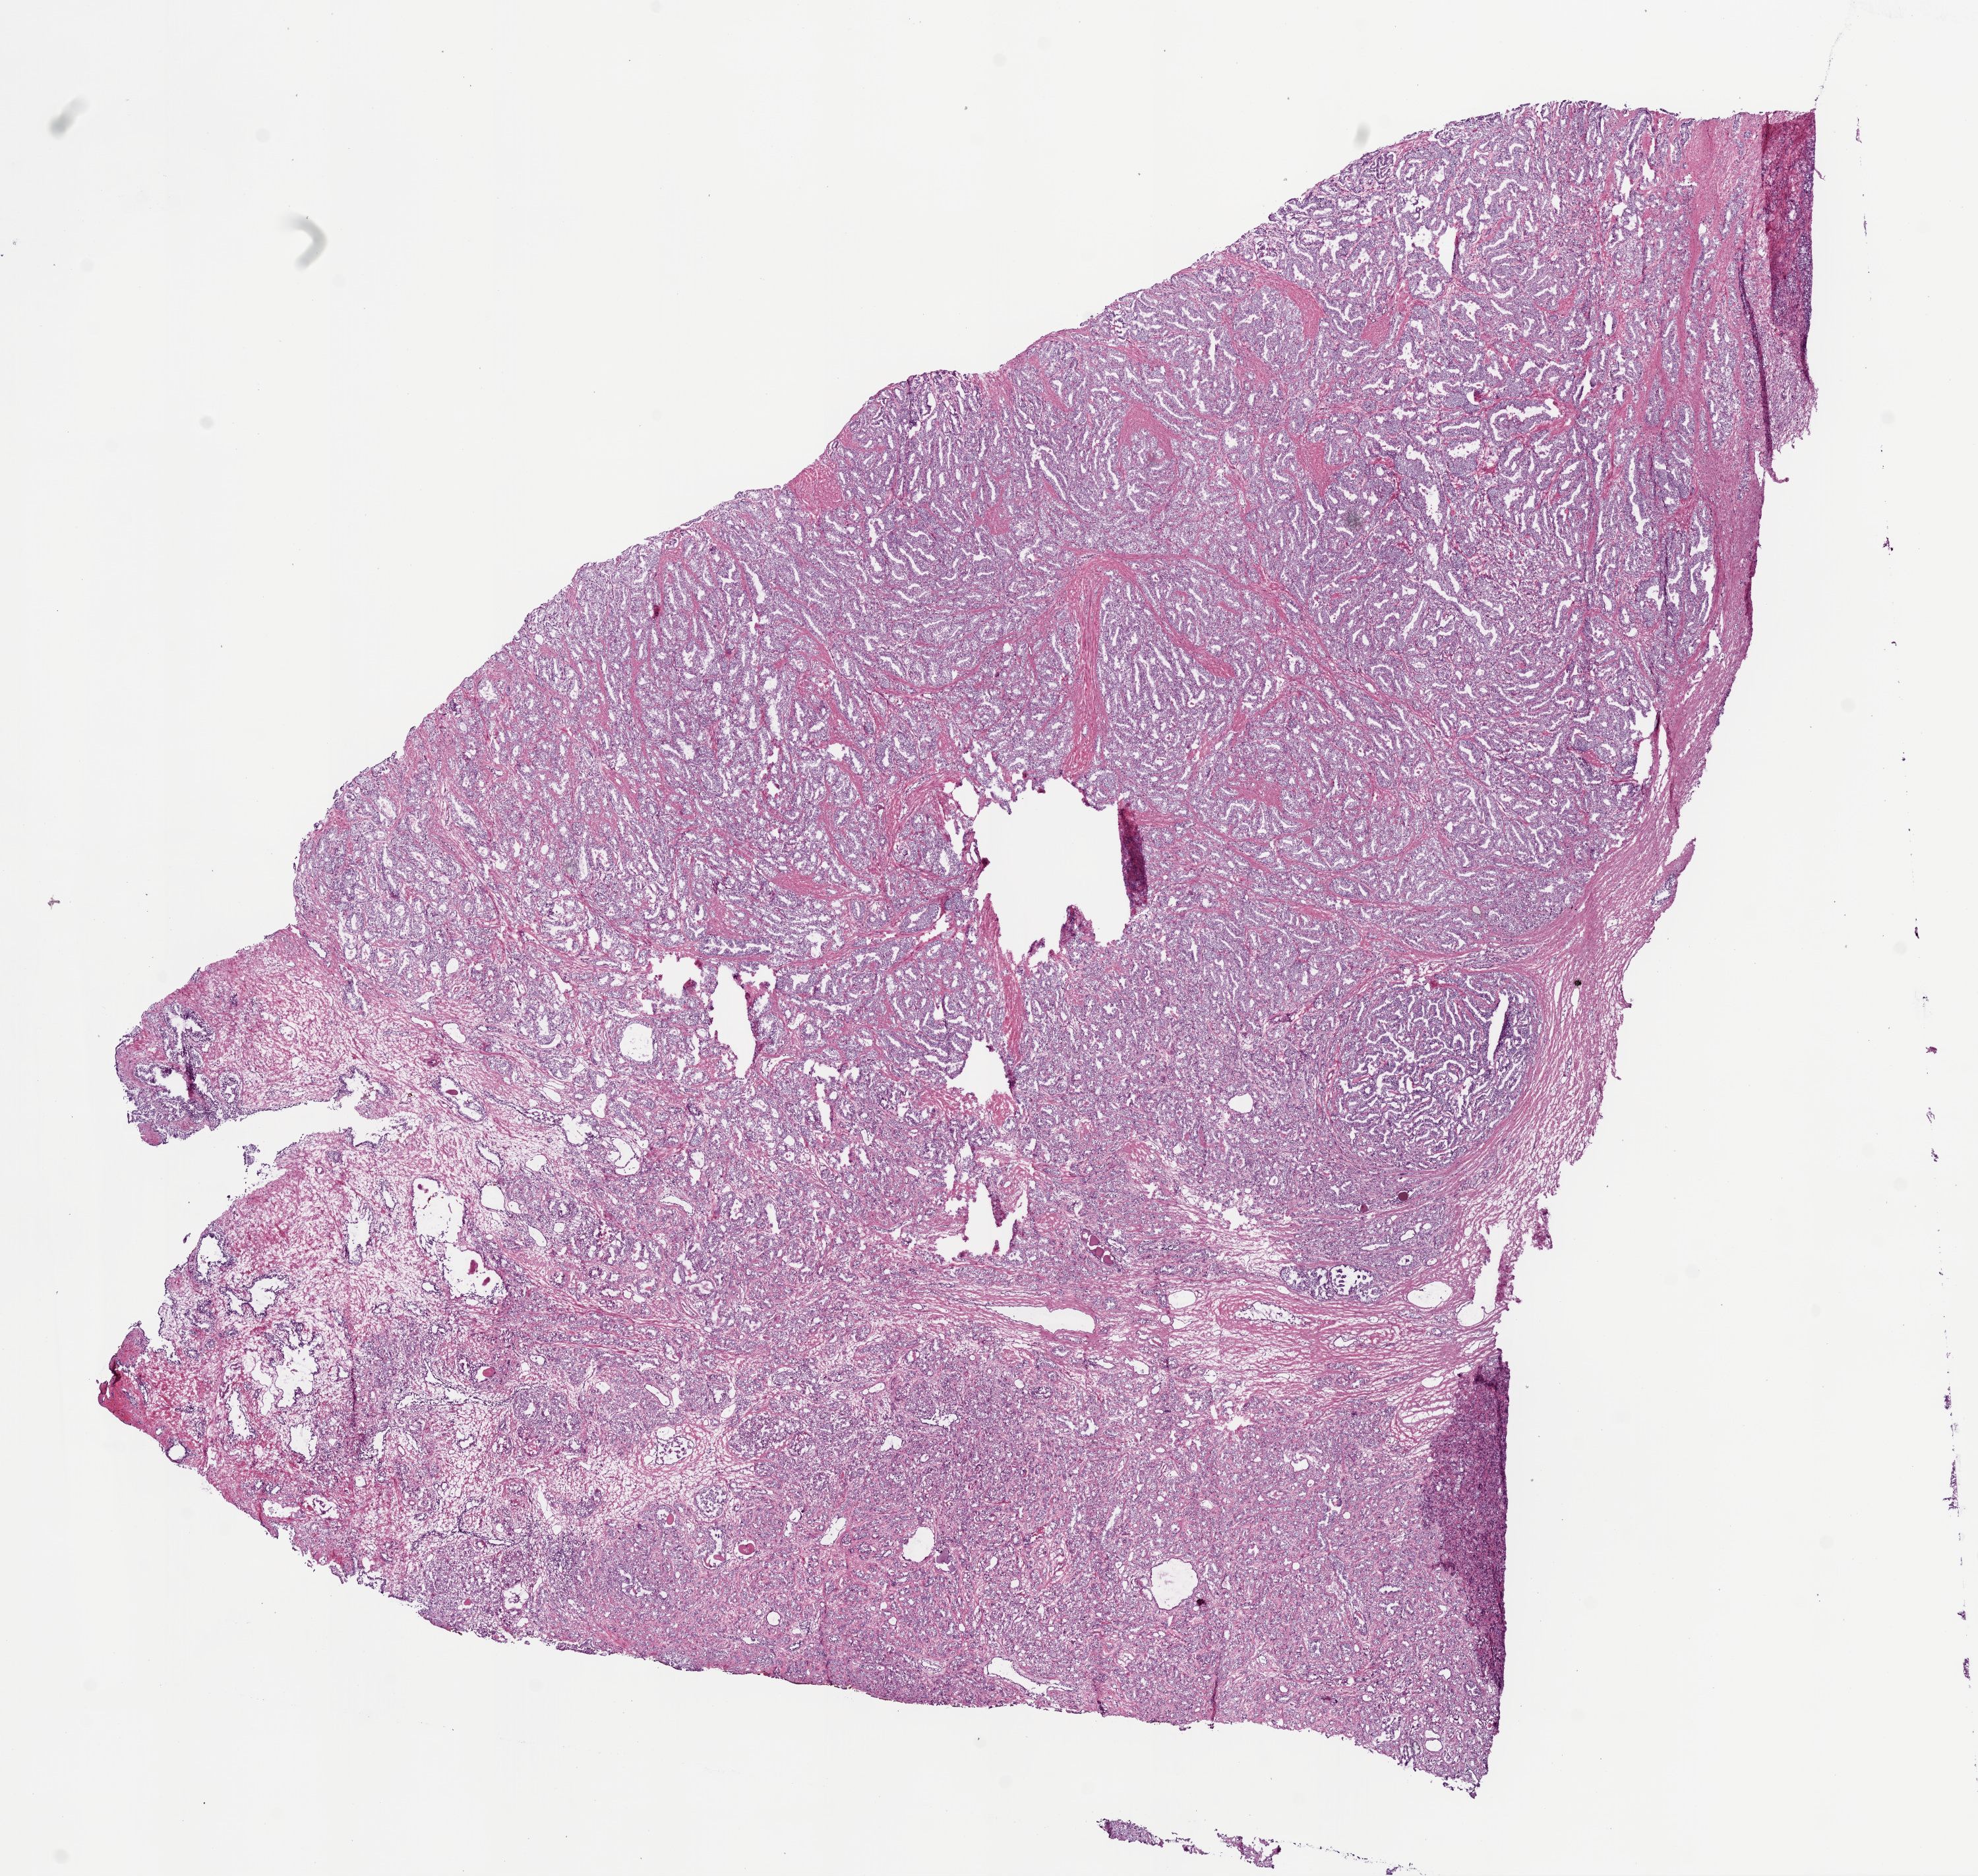
Whole-slide histology image, Hematoxylin and eosin (H&E) stained, shown as a low-resolution overview of the whole scanned area (about 12.0 x 11.4 mm, acquisition: 20x scan). Frozen section from the bottom of the tissue portion. Primary tumour sample from the prostate. Male, age 65 years at initial diagnosis. Gleason score: 7 (4+3). Slide review estimates, as recorded: tumour cells 70%, tumour nuclei 85%, normal cells 10%, stromal cells 20%, necrosis 0%. Infiltration values recorded for this section: lymphocyte infiltration 0%, monocyte infiltration 0%, neutrophil infiltration 0%.
- histologic diagnosis: Acinar cell carcinoma (prostate gland)
- lymph nodes positive (case pathology): 1 of 18 examined